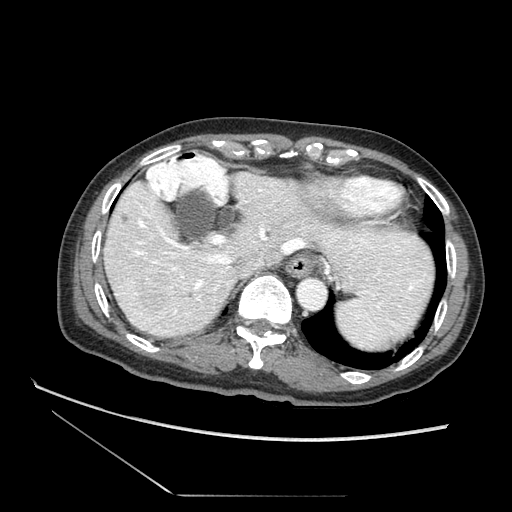
Contrast-enhanced abdominal CT (liver protocol), one axial slice. Position 60 of 73 along the scan axis. Reconstruction kernel STANDARD. Soft-tissue window (W 400 / L 40 HU). 2.5 mm slice thickness. 512 × 512 image matrix. From the clinical record (not read from this slice): diagnosis: hepatocellular carcinoma (patient treated with transarterial chemoembolisation; whether this scan precedes or follows treatment is not stated here); TNM stage (as recorded): Stage-II; Child-Pugh class: A; tumour nodularity: multinodular; tumour size: 3.8 cm.
Annotated regions visible in this slice (semi-automatic segmentation, software-assisted and operator-edited):
- abdominal aorta: box from (x=299, y=279) to (x=328, y=310) px
- liver parenchyma outside the tumour (the mass and vessels are separate outlines, so this box may not span the whole liver): (x=98, y=170)–(x=441, y=345)
- mass: (x=118, y=265)–(x=178, y=316)
- liver vessels: (x=99, y=188)–(x=398, y=285)